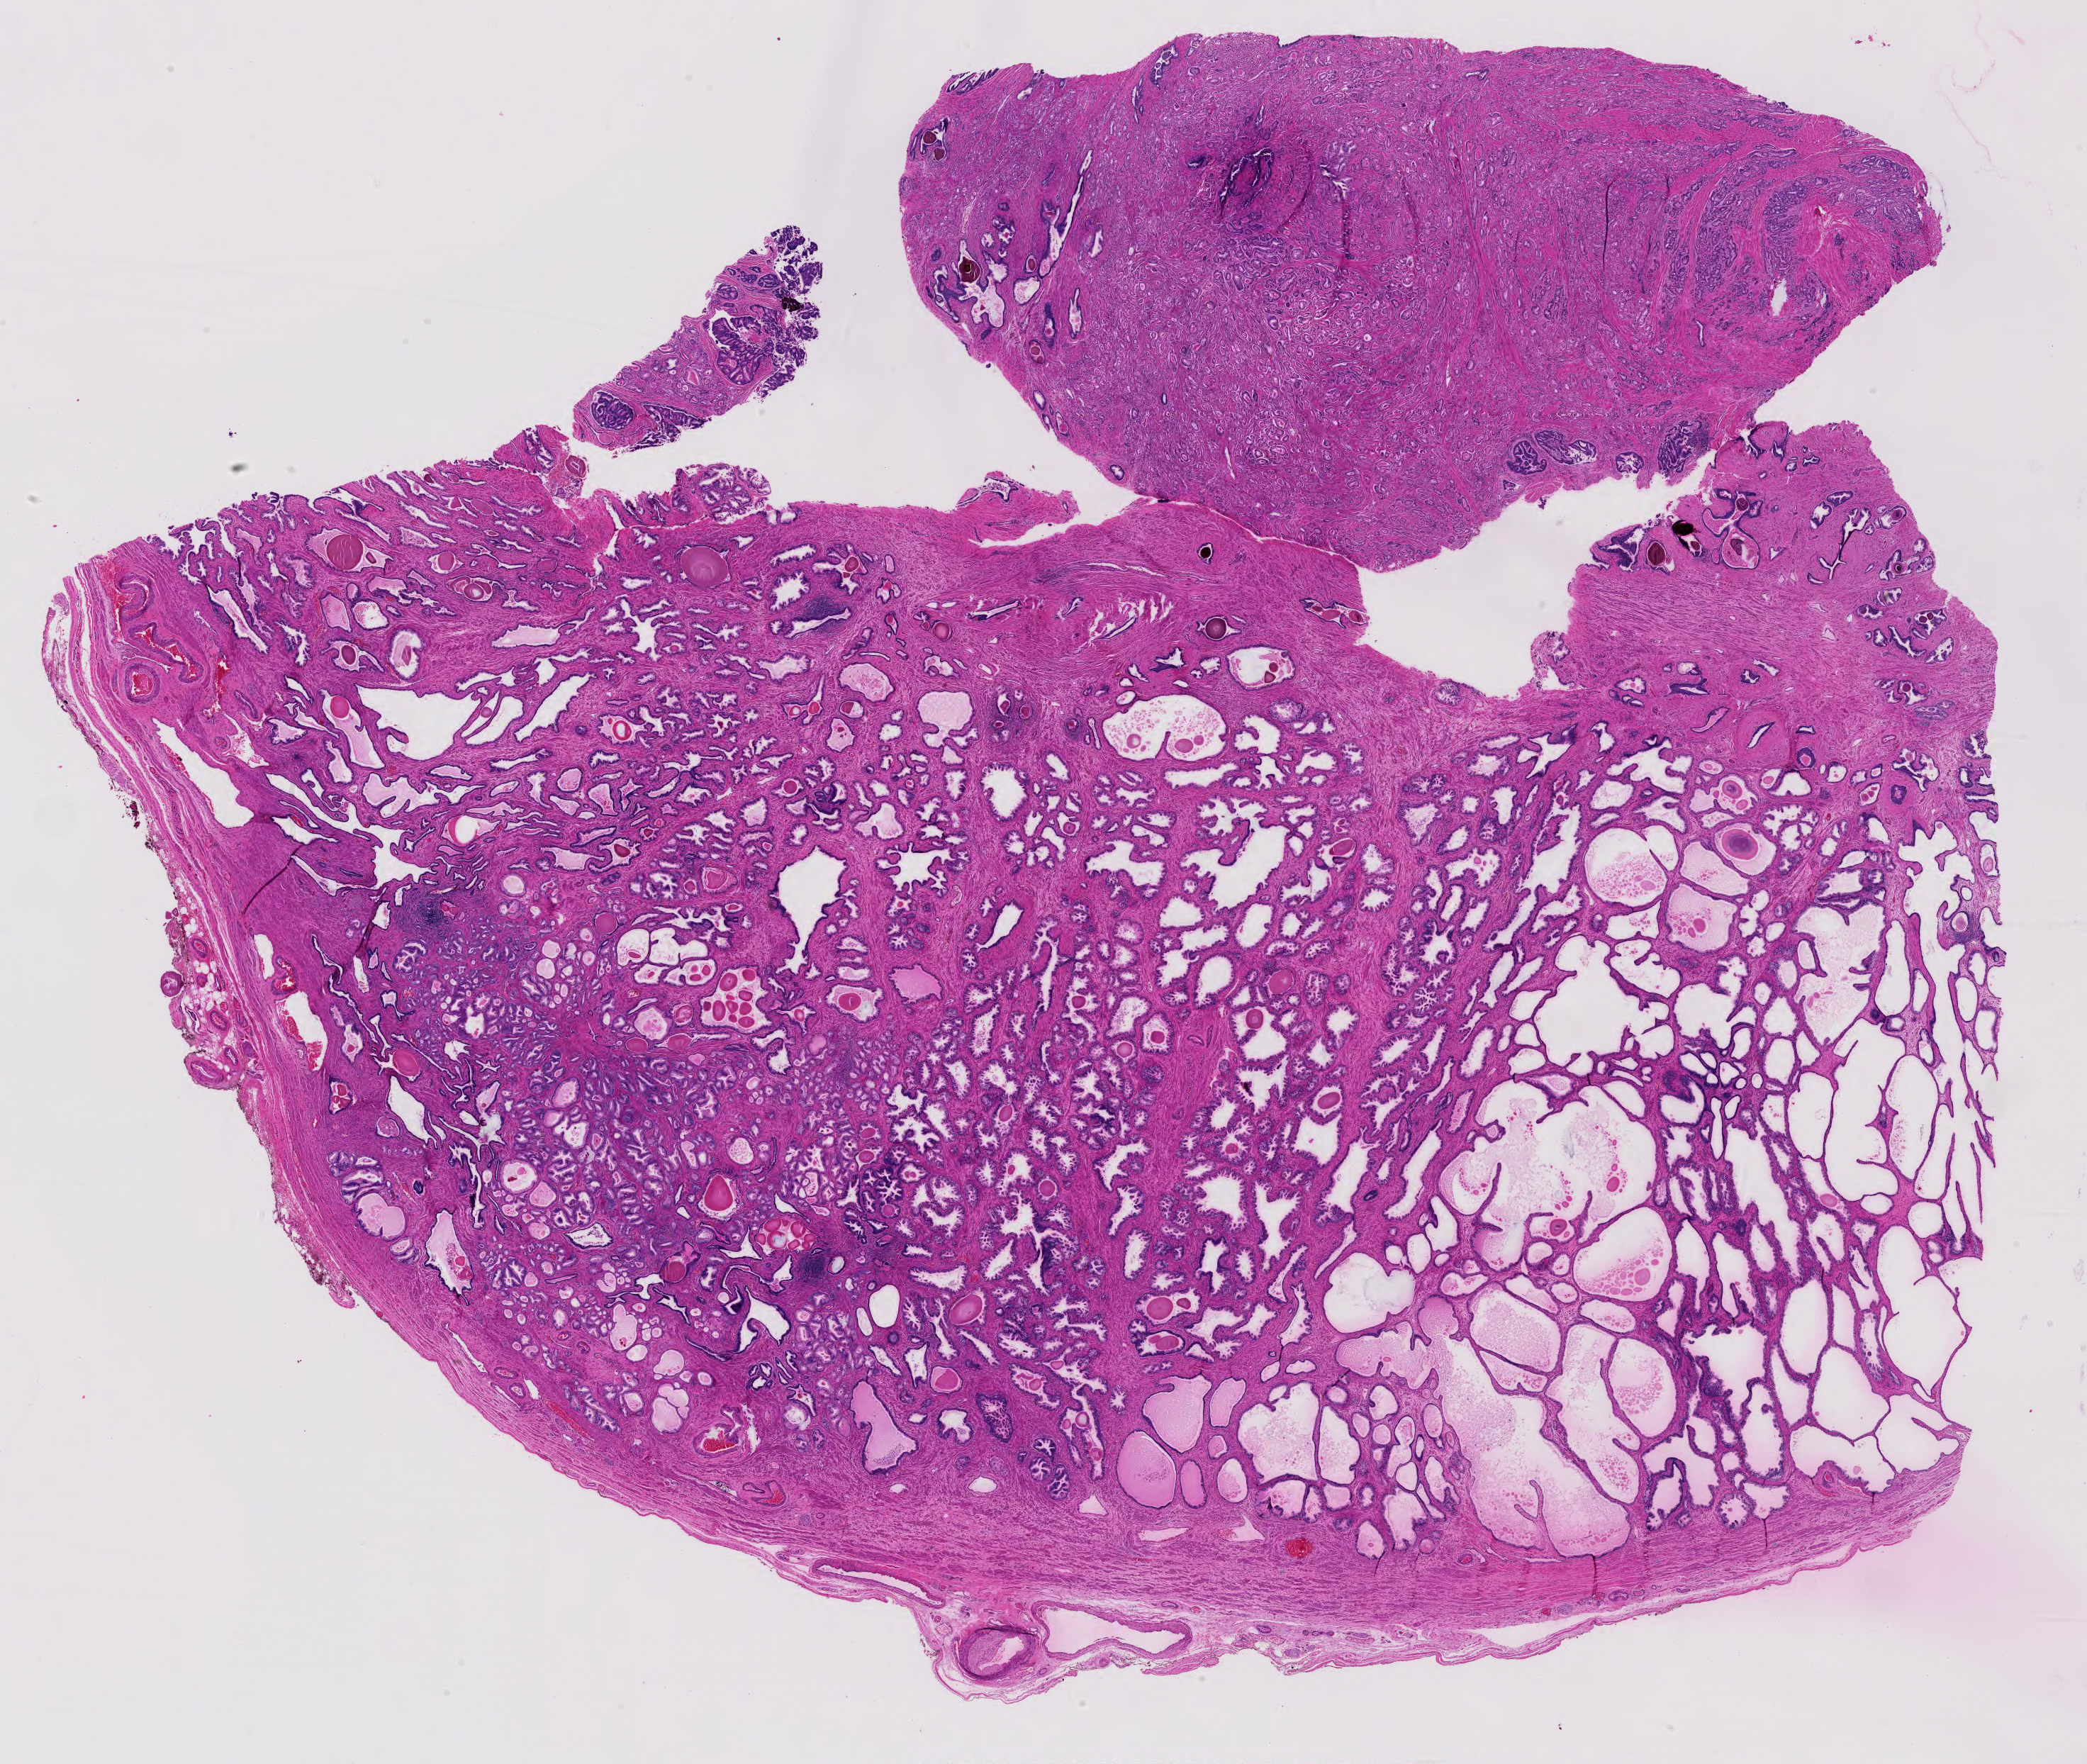
H&E-stained whole-slide image, shown as a low-resolution overview of the whole scanned area (about 21.4 x 18.0 mm, acquisition: 40x scan). Formalin-fixed paraffin-embedded (FFPE) diagnostic section. Prostate, primary tumour sample. Patient: male, age at initial diagnosis 63 years.
Histologic diagnosis: Adenocarcinoma, NOS (prostate gland).